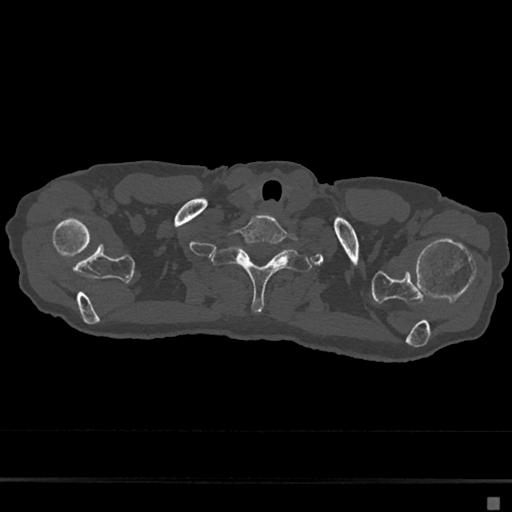
CT including the spine, one axial slice. Slice 619 of 797 in the series (ordered by position). Reconstruction kernel Br40s/3. Bone window (W 1800 / L 400 HU). 512 × 512 image matrix, field of view 360 × 360 mm. Female patient, age 68 years. From the clinical record (not read from this slice): primary cancer: renal.
Structures marked on this image (semi-automatic segmentation, software-assisted and operator-edited):
- T1 vertebra: box from (x=212, y=247) to (x=312, y=312) px